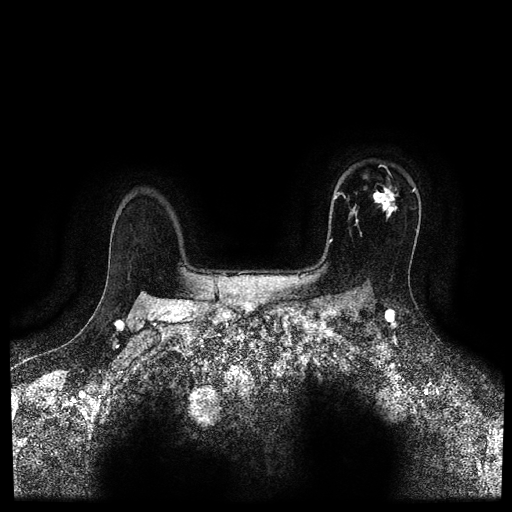
Breast MRI (dynamic contrast-enhanced, multi-phase), one axial slice. Slice 77 of 116 in the series (ordered by position). Dynamic contrast-enhanced series, time point 2 of 5 at this slice position (early post-contrast). 1.5 T. TE 2.7 ms, TR 5.4 ms. 2 mm slice thickness. 512 × 512 image matrix. Female patient, age 50 years.
Outlined on this slice (semi-automatic segmentation, software-assisted and operator-edited):
- breast lesion (labelled 'tumour' in the annotation; benign lesions carry a separate 'benign' label): box from (x=370, y=183) to (x=403, y=219) px